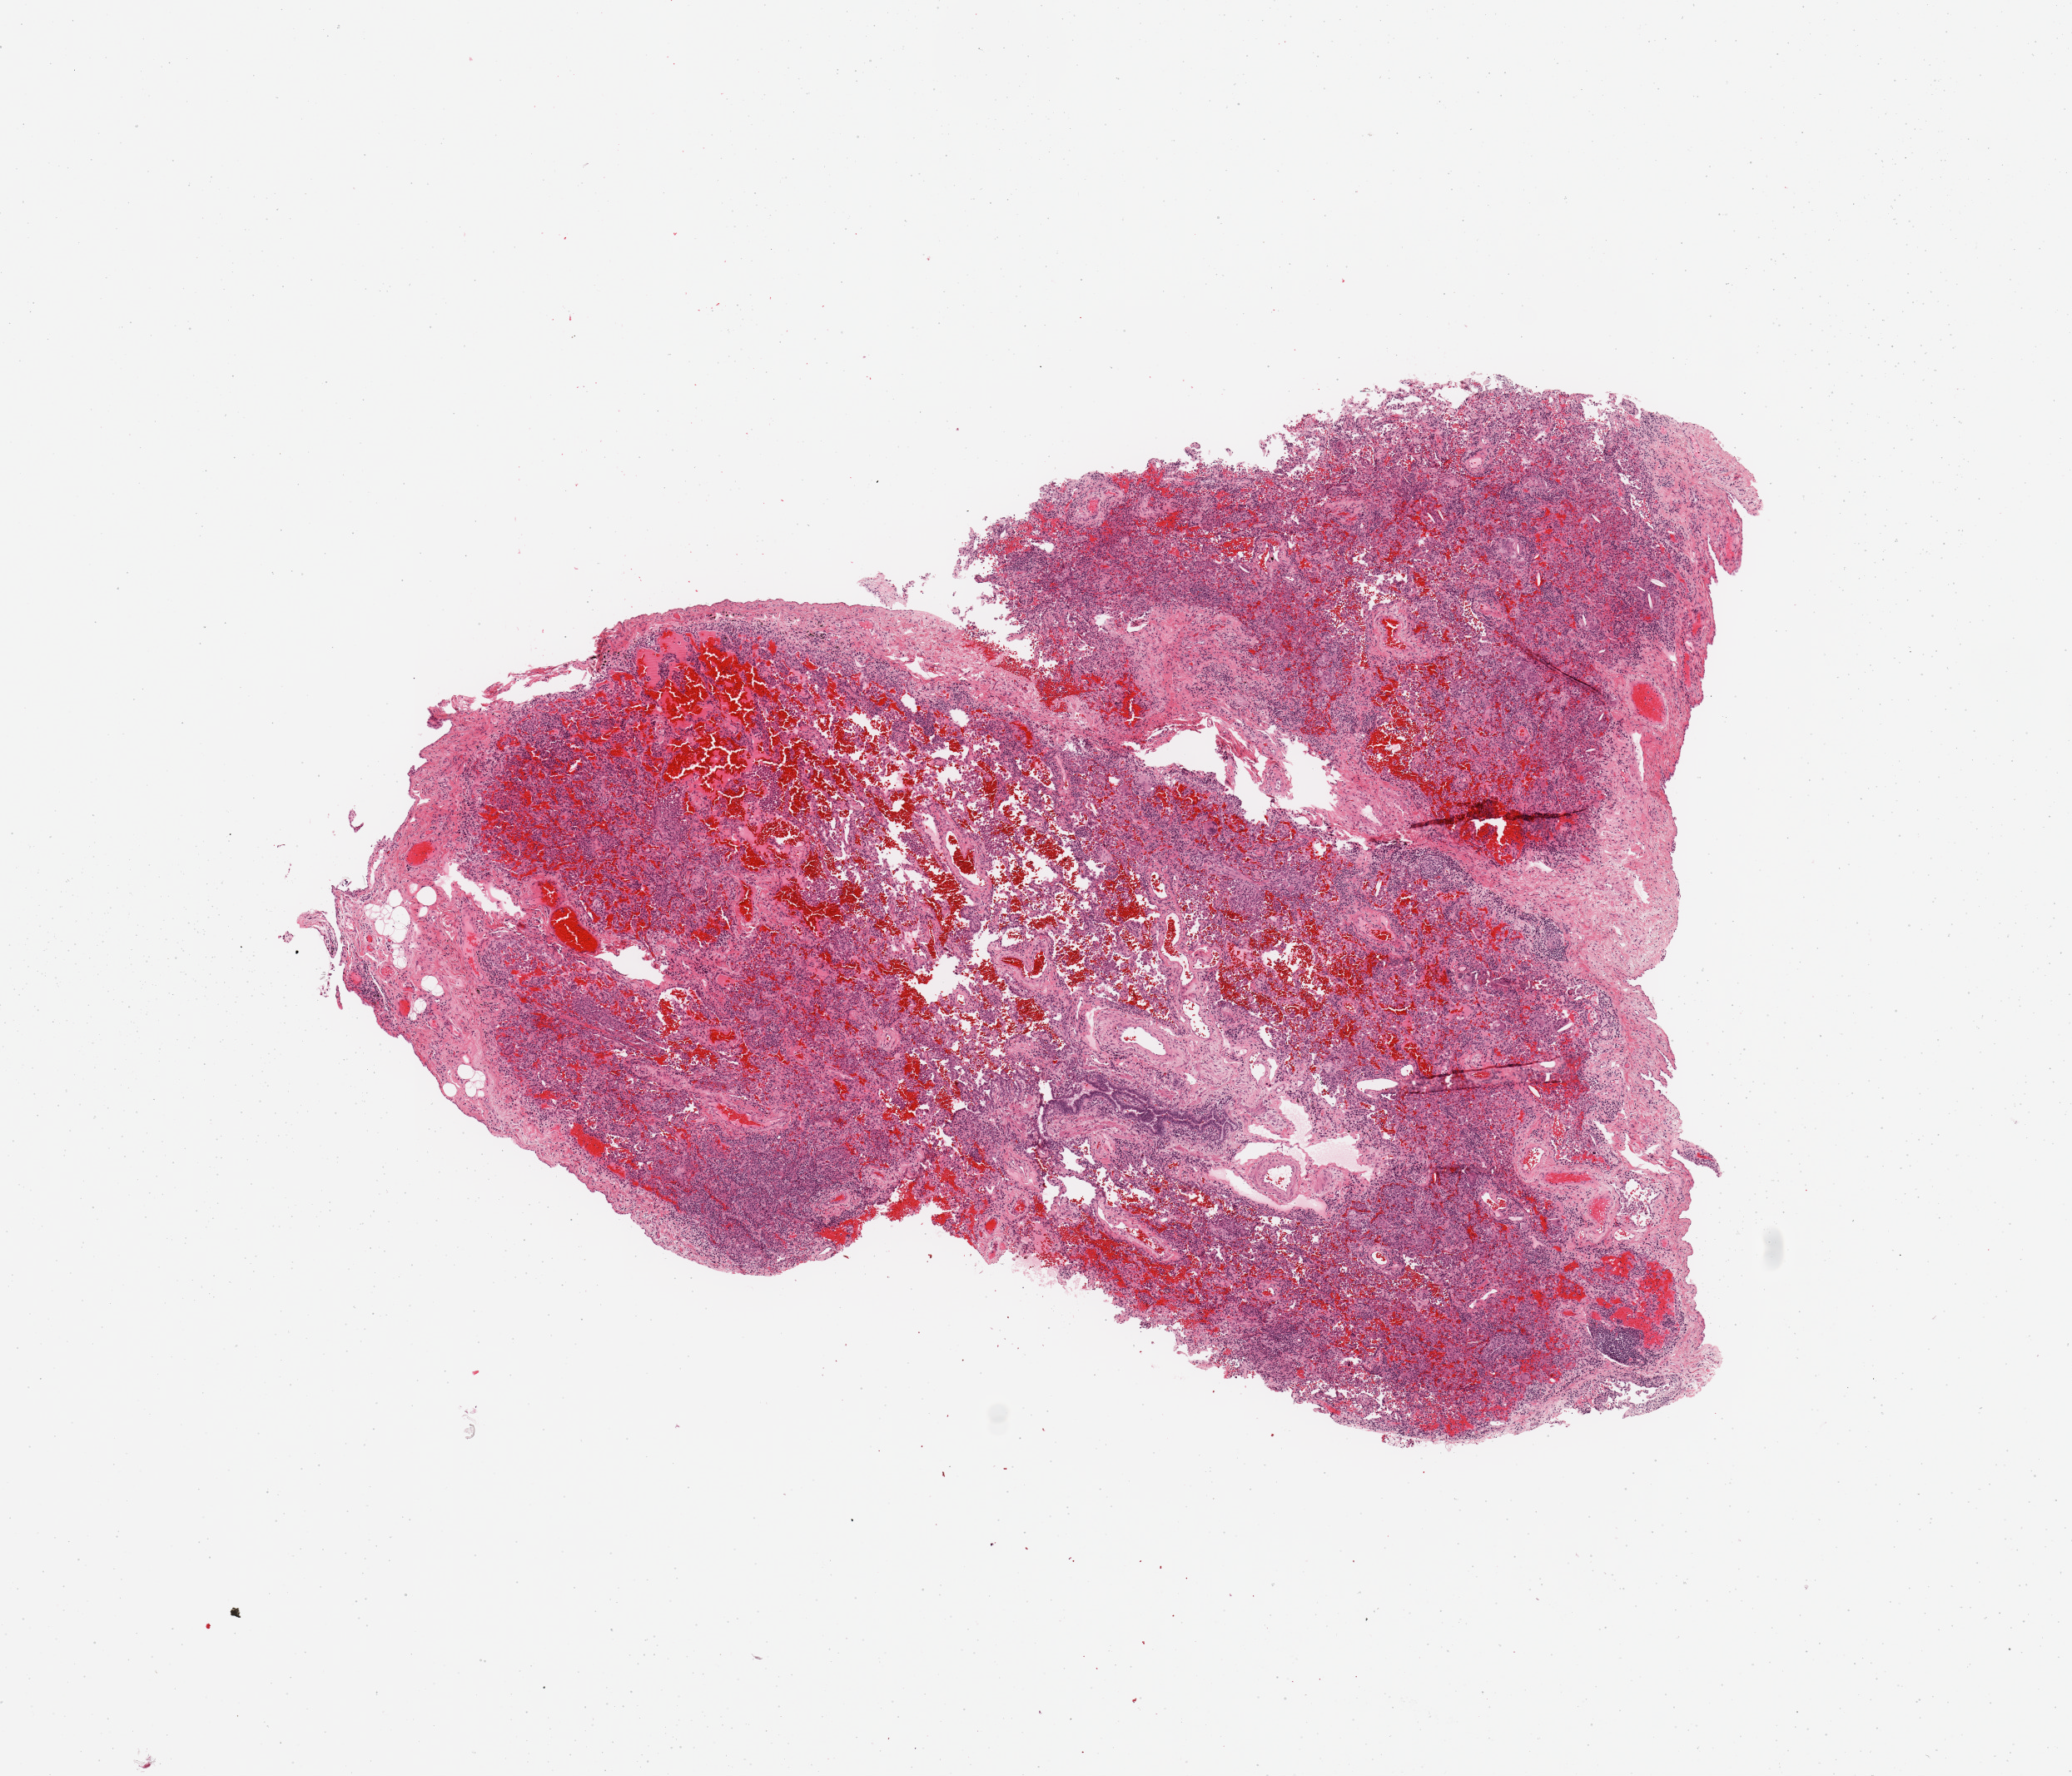
Whole-slide histology image, H&E-stained — whole scanned area (about 9.8 x 8.4 mm) shown as a low-resolution overview, normal (non-tumour) tissue sample, sampled site: lung. Patient: male, age 58 years.
This section: normal (non-tumour) tissue from the same patient. Patient diagnosis: Squamous cell carcinoma, NOS.